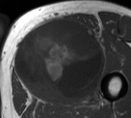
MRI of an extremity soft-tissue mass, one axial slice. Slice 38 of 55 in the series (ordered by position). MR volume resampled by the dataset authors to the PET/CT grid (not the native acquisition matrix). 131 × 118 image matrix. Male patient. Case-level facts recorded for this patient, not image findings: histological type: pleiomorphic liposarcoma; grade: high; site of the primary tumour: left thigh.
Structures marked on this image (expert contour drawn on MRI and transferred to this co-registered scan by the dataset authors):
- gross tumour volume including surrounding oedema: bounding box (x1, y1, x2, y2) in pixels: (16, 18, 106, 99)
- gross tumour volume (mass): (16, 18, 103, 99)